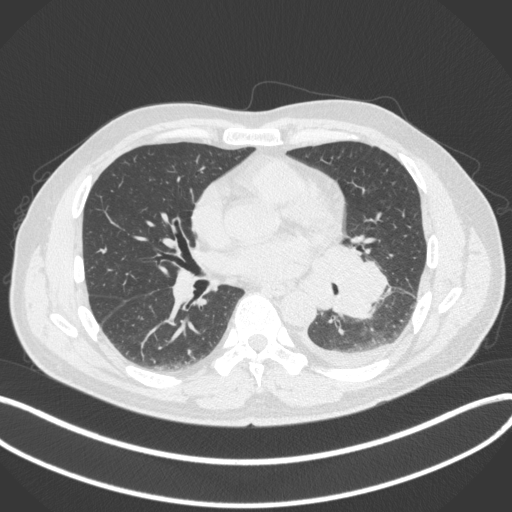
Chest CT, one axial slice; position 176 of 350 along the scan axis; lung window (W 1500 / L -600 HU); 512 × 512 image matrix, field of view 400 × 400 mm. Male patient, age 58 years. From the clinical record (not read from this slice): clinical TNM (as recorded): T3 N1 M1b; histopathological grade: G3.
Outlined on this slice (bounding box drawn by a radiologist):
- lung tumour (recorded histology: small cell carcinoma): bounding box [x1, y1, x2, y2] px = [309, 236, 392, 321]